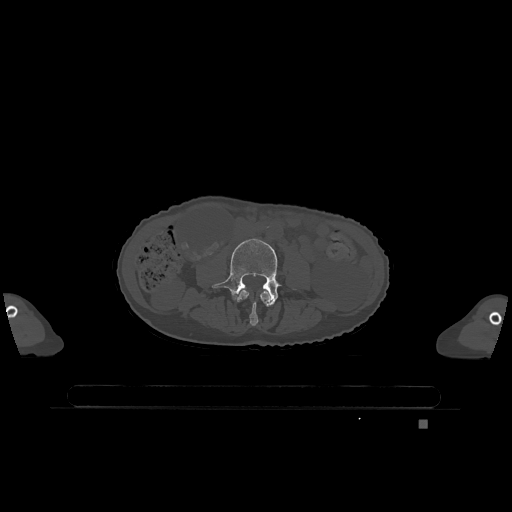
CT including the spine, one axial slice; slice 315 of 1317 in the series (ordered by position); bone window (W 1800 / L 400 HU); 0.5 mm slice thickness; 512 × 512 image matrix, field of view 500 × 500 mm. Patient: female, 74 years. From the clinical record (not read from this slice): primary cancer: lung.
Structures marked on this image (semi-automatically segmented with operator editing):
- L3 vertebra: bounding box [x1, y1, x2, y2] px = [239, 290, 271, 326]
- L4 vertebra: [211, 238, 294, 305]